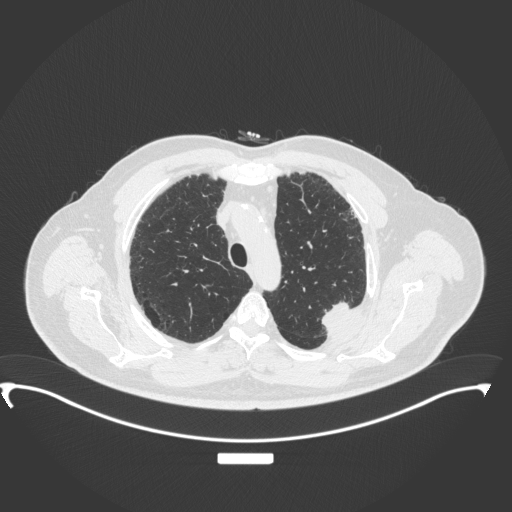
Chest CT, one axial slice. Slice 280 of 350 in the series (ordered by position). Reconstruction kernel B31f. 120 kVp. Lung window (W 1500 / L -600 HU). 1 mm slice thickness. 512 × 512 image matrix, field of view 459 × 459 mm. Male patient, age 64 years. From the clinical record (not read from this slice): clinical TNM (as recorded): T1c N1 M1.
Outlined on this slice (bounding box drawn by a radiologist):
- lung tumour (recorded histology: adenocarcinoma): box from (x=316, y=297) to (x=354, y=329) px